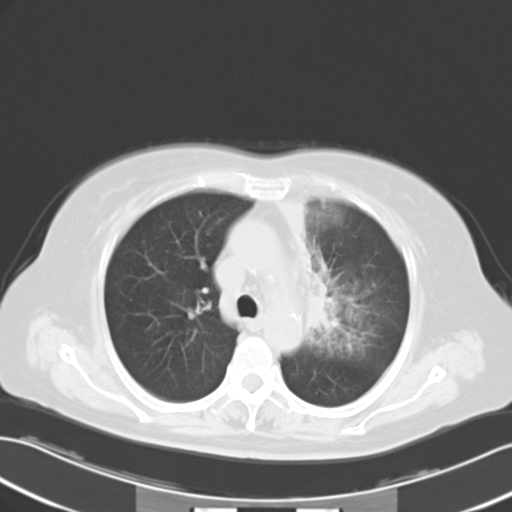
Chest CT, one axial slice. Reconstruction kernel B40f. 120 kVp. Lung window (W 1500 / L -600 HU). 10 mm slice thickness. 512 × 512 image matrix, field of view 353 × 353 mm. Patient: female, 65 years. From the clinical record (not read from this slice): clinical TNM (as recorded): T2b N1 M0.
Outlined on this slice (rectangle marked by the reading radiologist):
- lung tumour (recorded histology: adenocarcinoma): bounding box <308,273,337,338> (left, top, right, bottom; pixels)